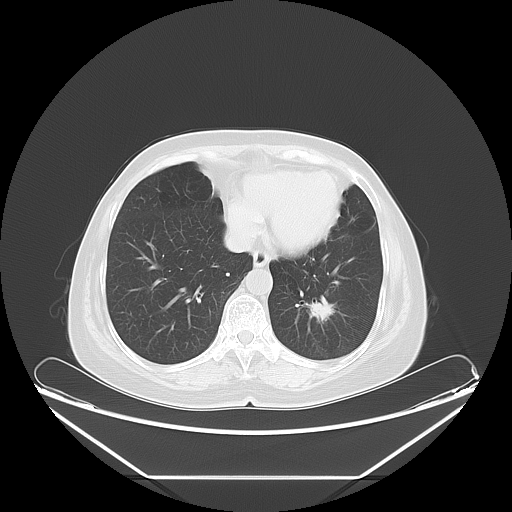
Chest CT, one axial slice; position 20 of 61 along the scan axis; reconstruction kernel LUNG; lung window (W 1500 / L -600 HU); 5 mm slice thickness; 512 × 512 image matrix. Patient: female, 63 years. From the clinical record (not read from this slice): clinical TNM (as recorded): T1c N0 M0; histopathological grade: G2-3.
Outlined on this slice (rectangle marked by the reading radiologist):
- lung tumour (recorded histology: adenocarcinoma): bounding box [x1, y1, x2, y2] px = [300, 286, 337, 330]